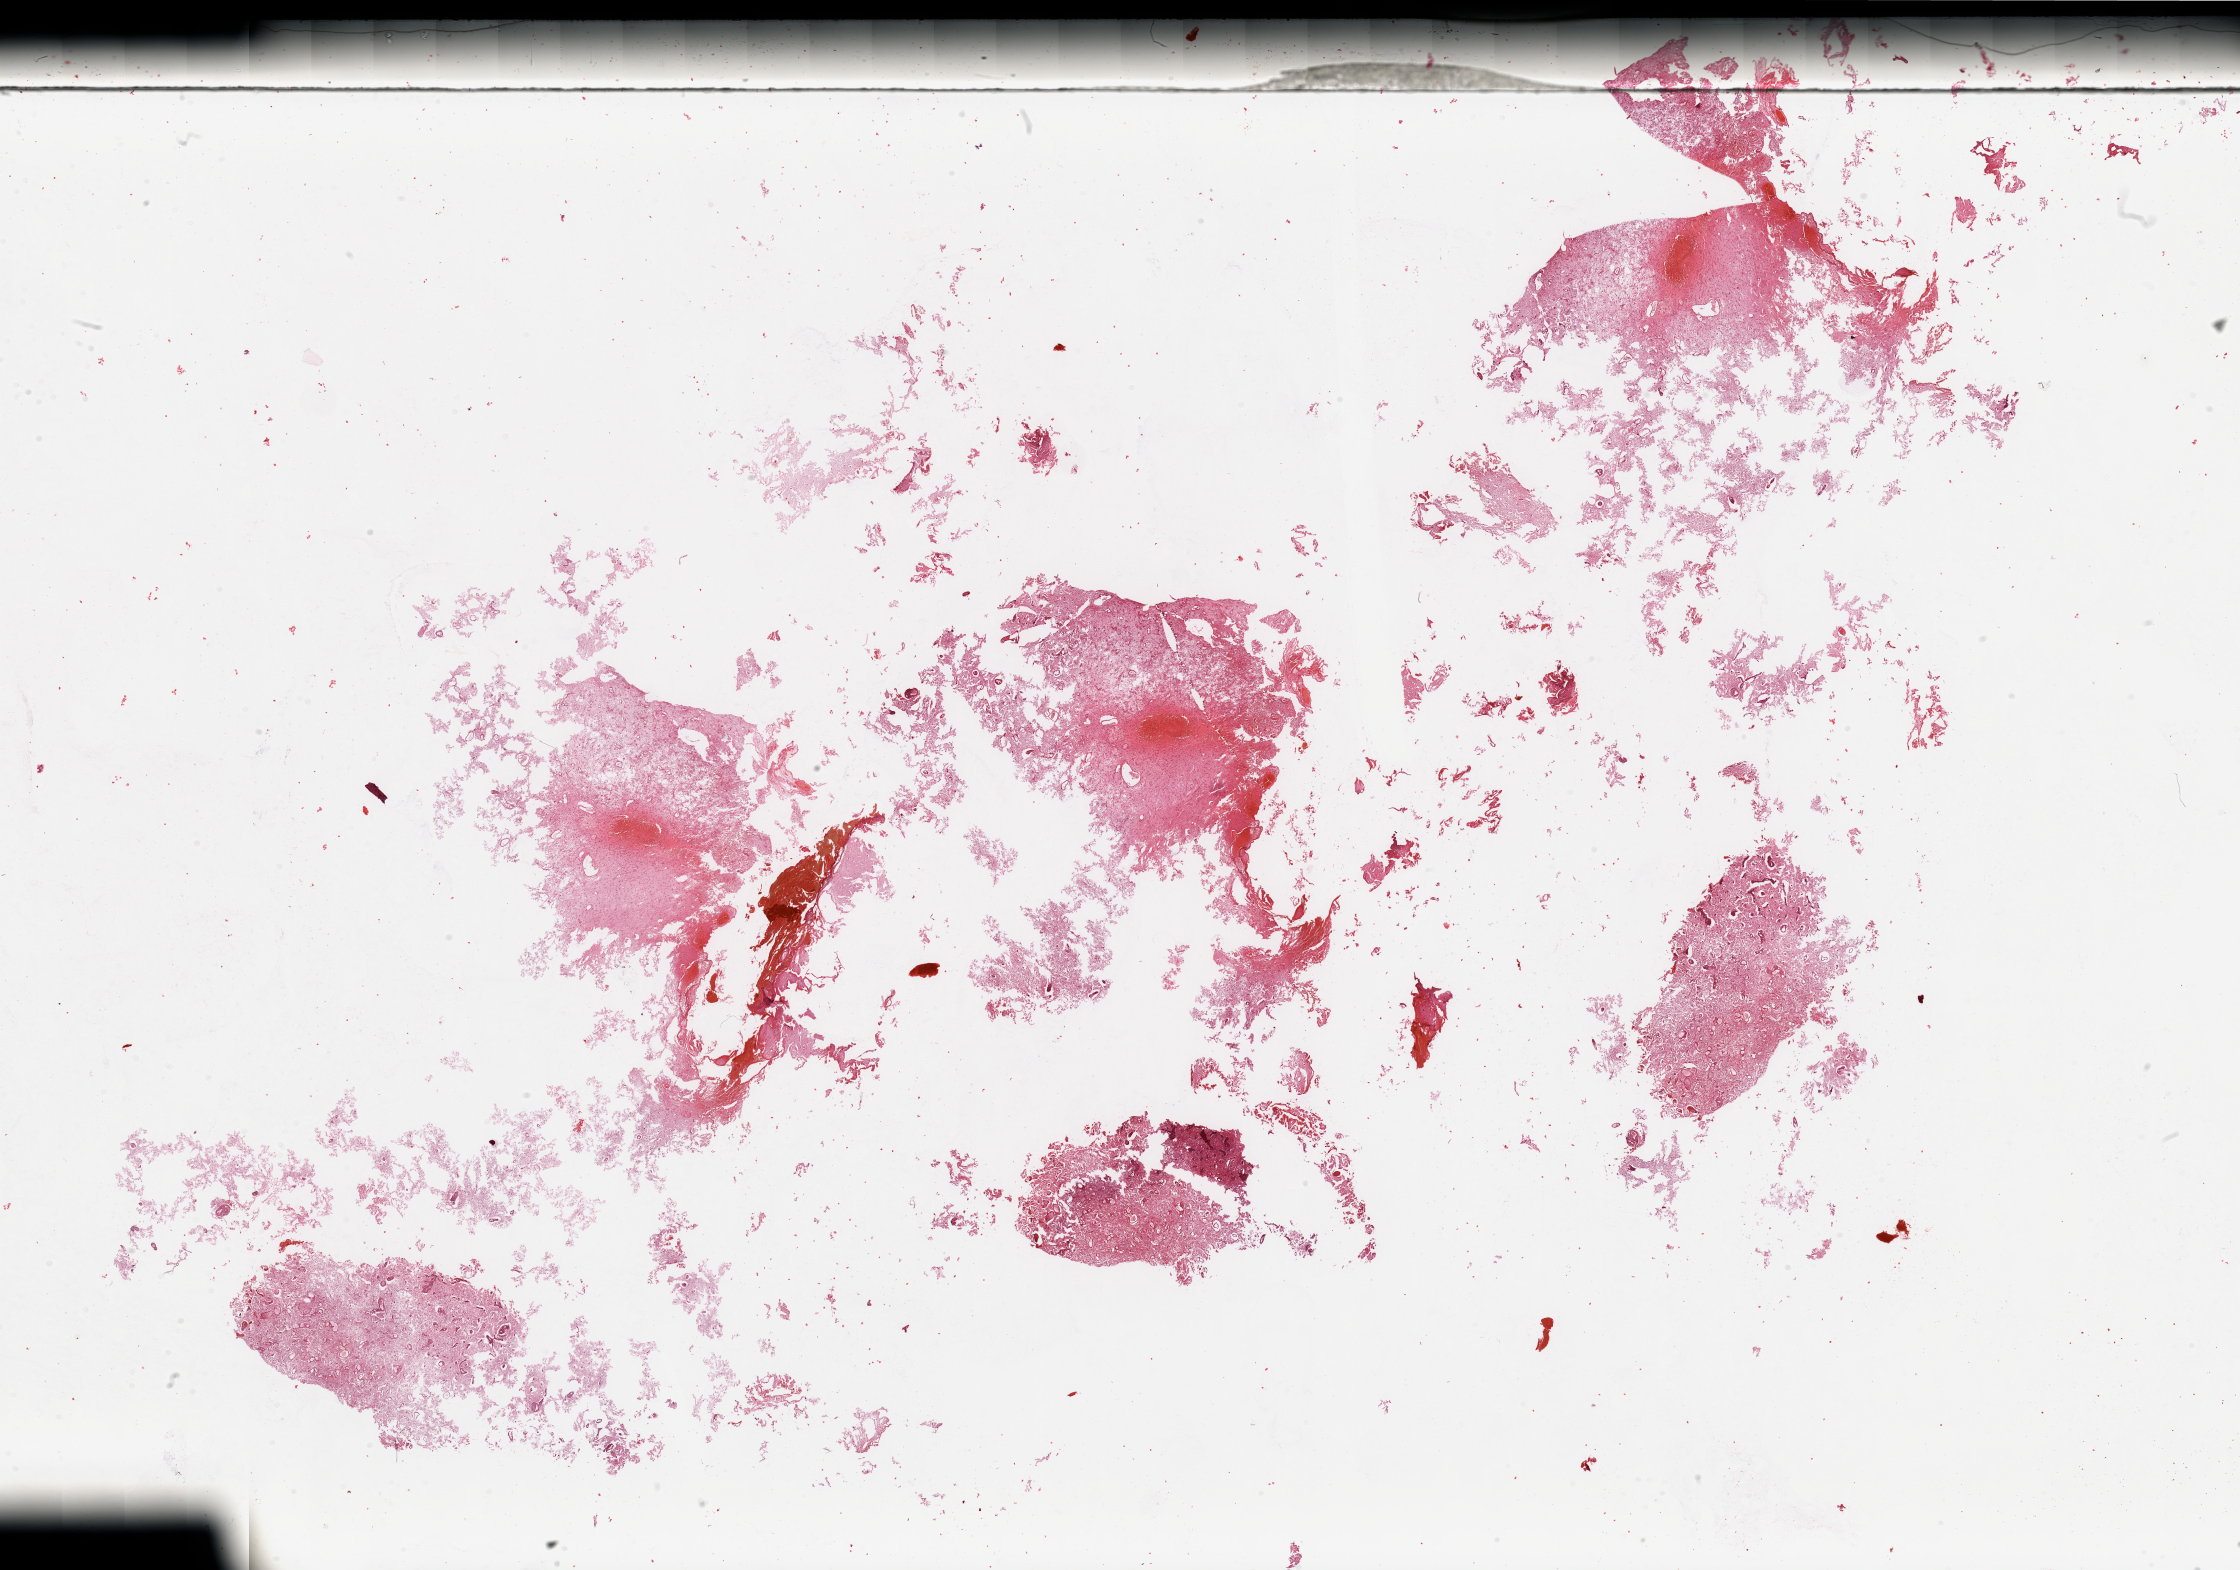
Digitized H&E tissue section (whole slide) — low-resolution overview of the scanned area, about 35.4 x 24.8 mm. Brain, tumour tissue. Patient: female, age 65 years.
- histologic diagnosis: Glioblastoma
- primary tumour site (as recorded): frontal lobe